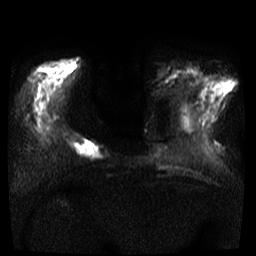
Breast MRI, one axial slice; position 8 of 35 along the scan axis; diffusion-weighted series; image 2 of 4 stored at this slice position (different b-values; order by instance number); 3 T; 5 mm slice thickness; 256 × 256 image matrix, field of view 300 × 300 mm. Female patient.
Annotated regions visible in this slice (outlined manually by an expert reader):
- tumour on diffusion-weighted imaging: bounding box <74,140,105,159> (left, top, right, bottom; pixels)